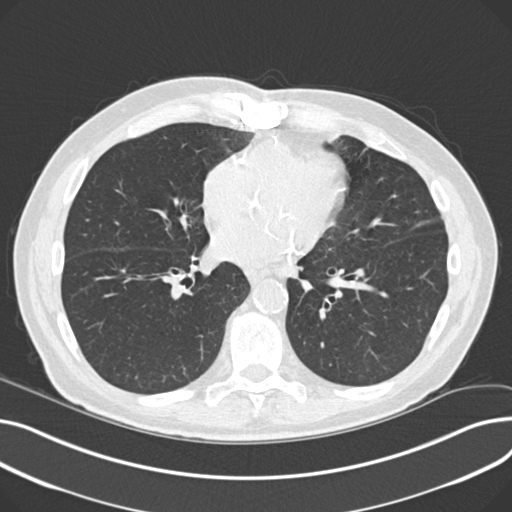
Low-dose screening chest CT, one axial slice; position 94 of 230 along the scan axis; reconstruction kernel B30f; 120 kVp; lung window (W 1500 / L -600 HU); 2 mm slice thickness; 512 × 512 image matrix.
Outlined on this slice (manually delineated by an expert):
- lesion 2 (tumor, lower lobe of right lung): bounding box (x1, y1, x2, y2) in pixels: (119, 268, 126, 274)